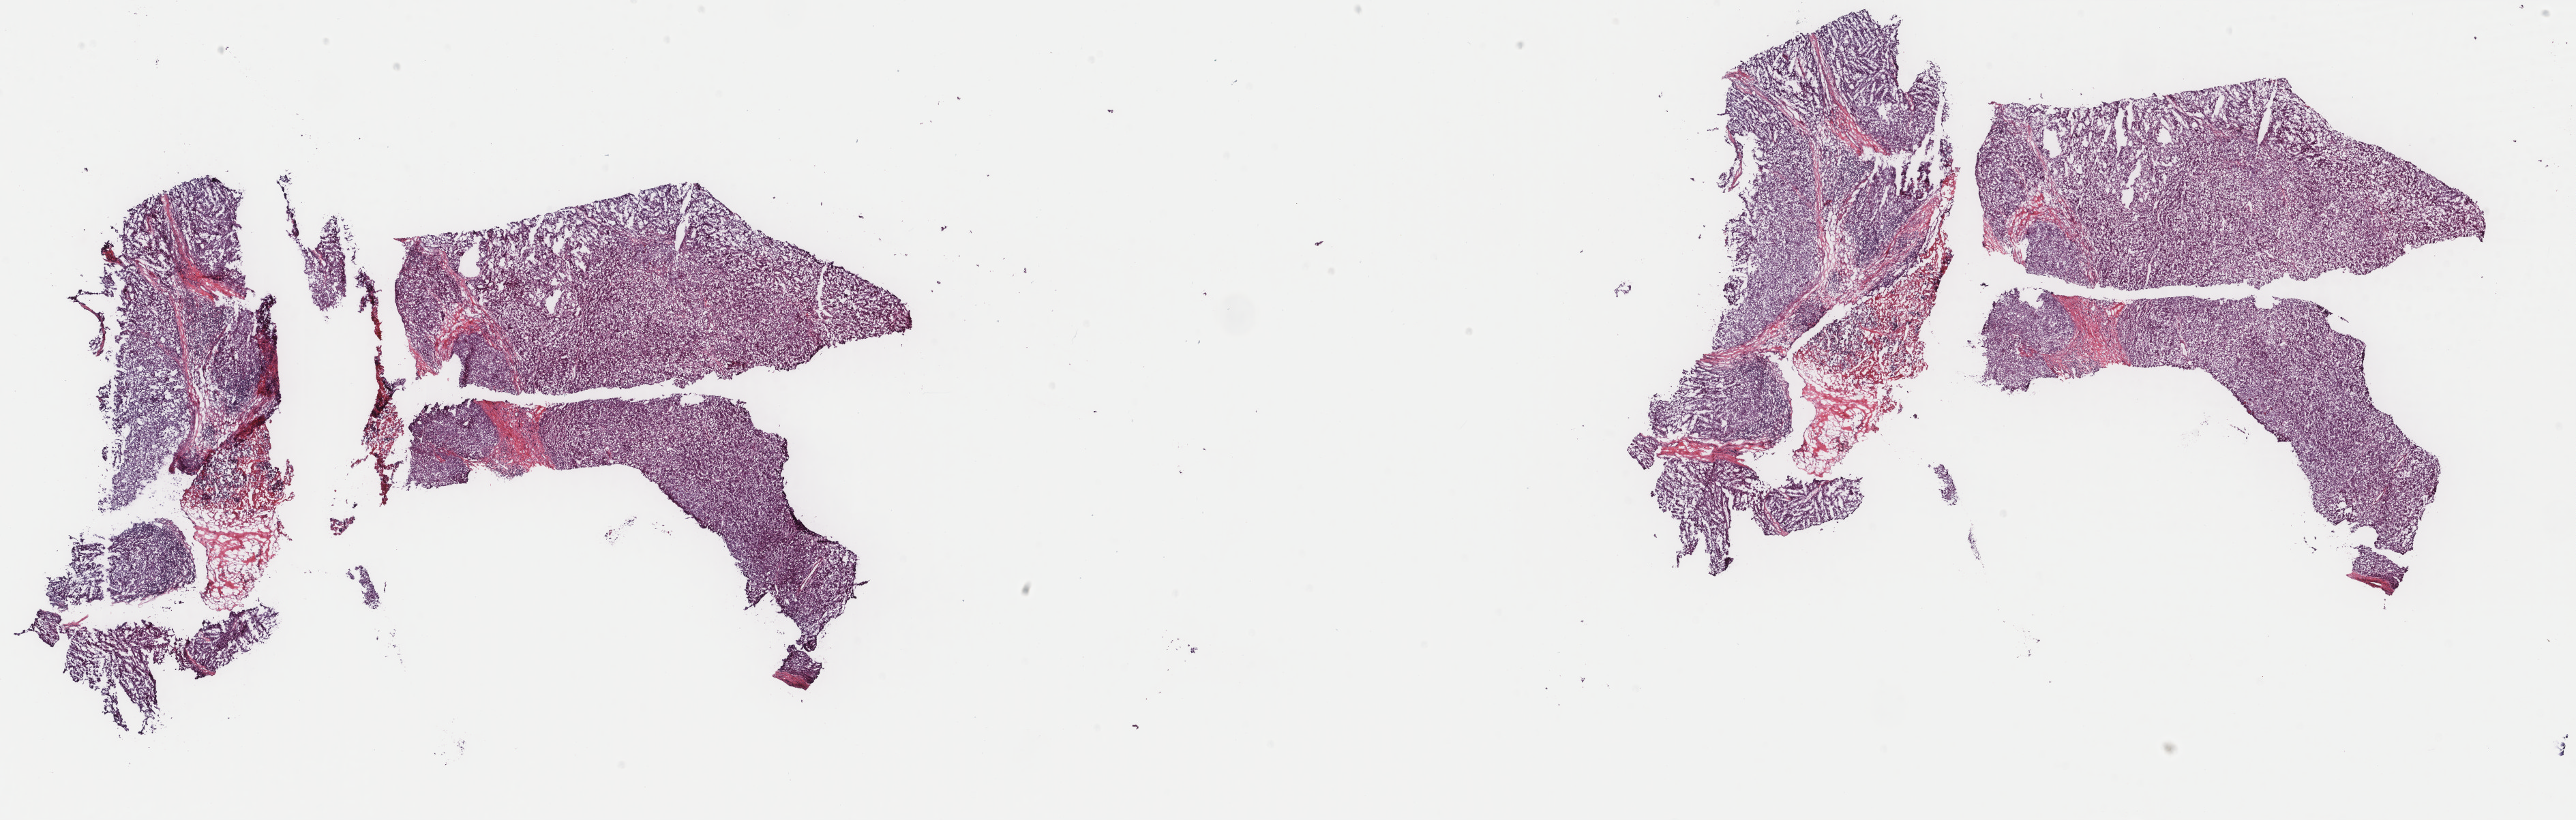
Whole-slide histology image, H&E-stained, low-resolution overview of the scanned area, about 30.0 x 9.5 mm (slide scanned at 40x). Frozen section from the top of the tissue portion. Sample: primary tumour, liver. Male, age 66 years at initial diagnosis. Histologic grade: G2 (moderately differentiated). Pathologist review of this section (percent, as recorded): tumour cells 100%, tumour nuclei 75%, normal cells 0%, stromal cells 0%, necrosis 0%. Infiltration values recorded for this section: lymphocyte infiltration 3%, monocyte infiltration 0%, neutrophil infiltration 0%.
Pathologic diagnosis: Hepatocellular carcinoma, NOS. AJCC pathologic stage: I (7th edition).